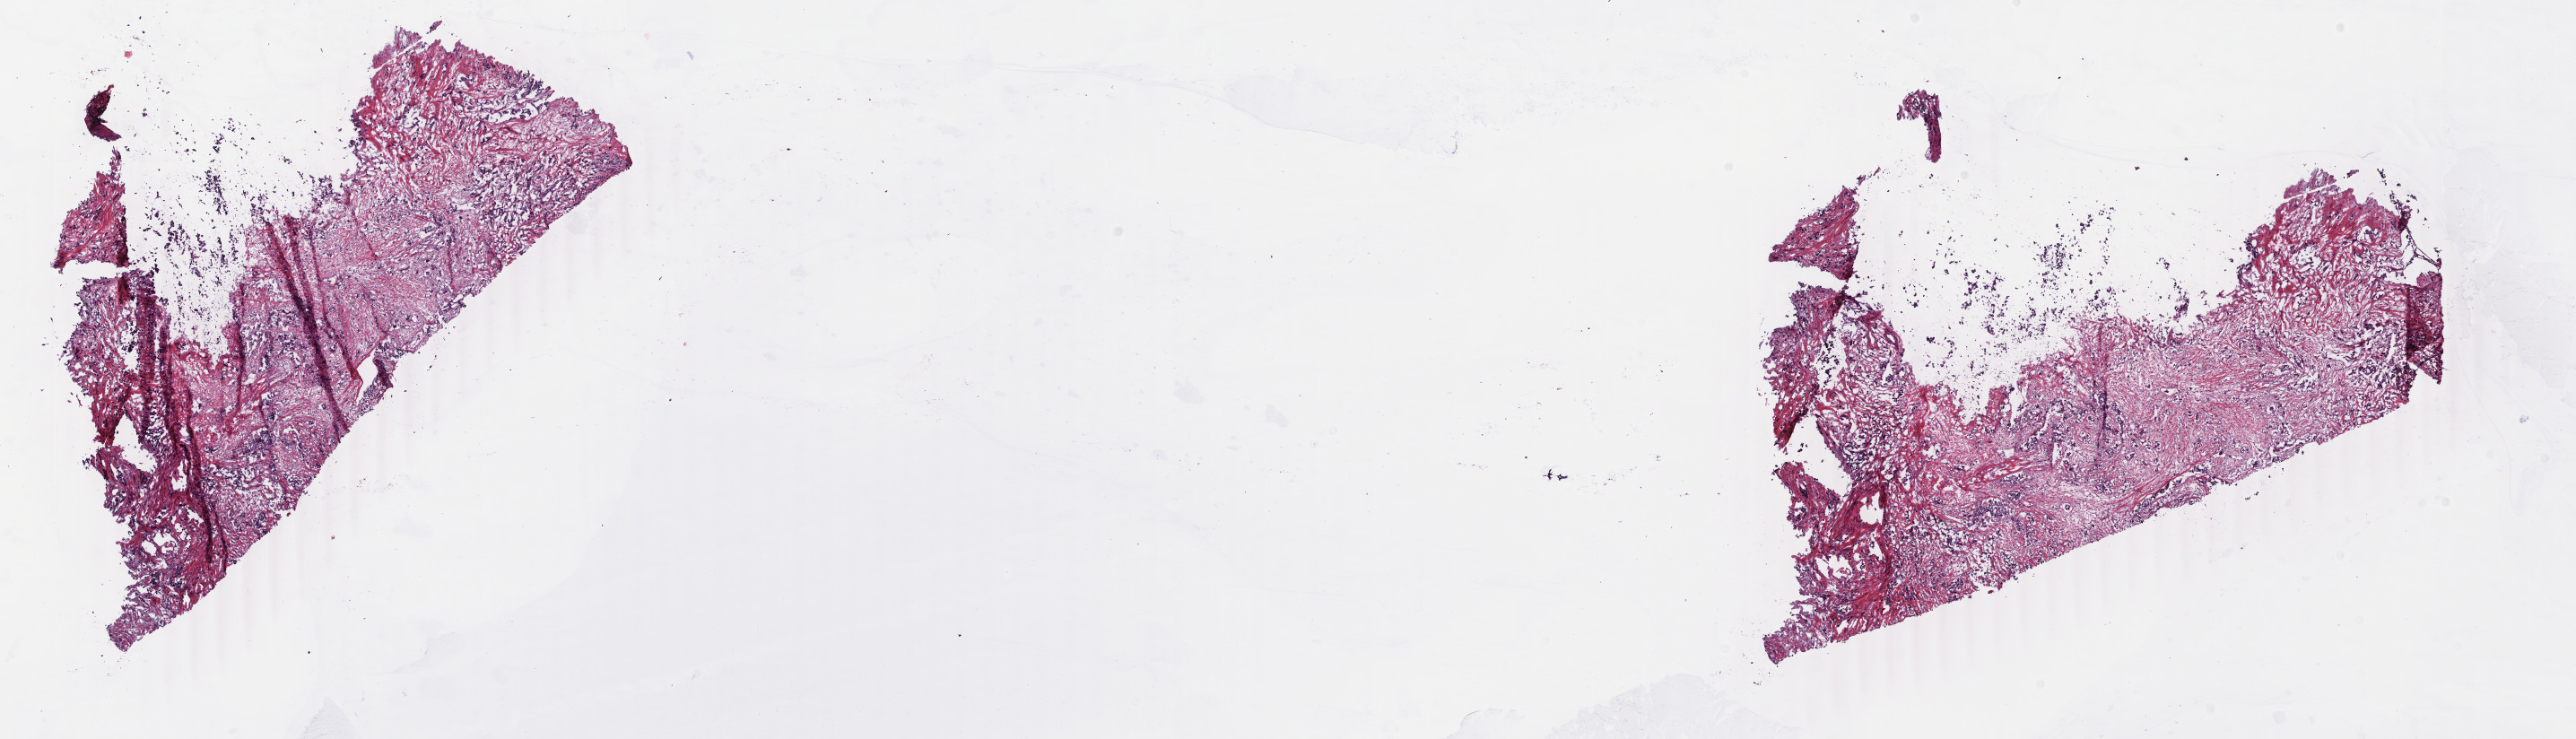
Whole-slide histology image, H&E, shown as a low-resolution overview of the whole scanned area (about 22.8 x 6.6 mm), frozen section from the bottom of the tissue portion, breast, primary tumour sample. Patient: female, age at initial diagnosis 50 years. Pathologist review of this section (percent, as recorded): tumour cells 60%, tumour nuclei 55%, normal cells 39%, stromal cells 0%, necrosis 1%. Inflammatory infiltration, as recorded: lymphocyte infiltration 1%, monocyte infiltration 0%, neutrophil infiltration 0%.
Diagnosis: Apocrine adenocarcinoma. AJCC pathologic stage: IIB.